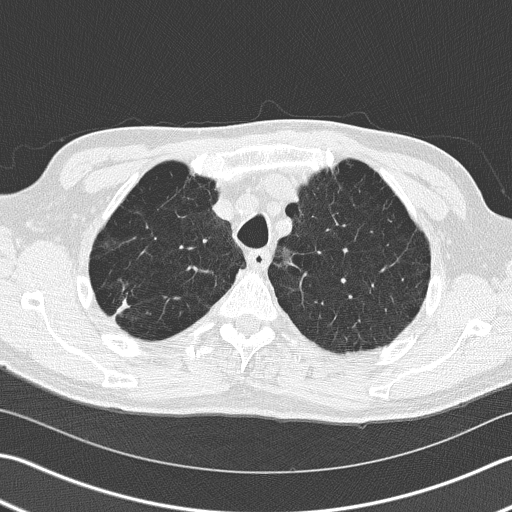
Low-dose screening chest CT, one axial slice; slice 129 of 163 in the series (ordered by position); reconstruction kernel B50f; 120 kVp; lung window (W 1500 / L -600 HU); 2 mm slice thickness; 512 × 512 image matrix.
Structures marked on this image (expert manual segmentation):
- lesion 1 (tumor, upper lobe of right lung): bounding box (x1, y1, x2, y2) in pixels: (118, 301, 128, 312)